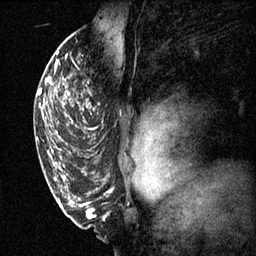
Breast MRI (dynamic contrast-enhanced), one sagittal slice. 3 images stored at this slice position (order not interpretable as contrast timing). 1.5 T. TE 4.2 ms, TR 11.1 ms. 256 × 256 image matrix, field of view 180 × 180 mm. Patient: female, 50 years.
Outlined on this slice (semi-automatically segmented with operator editing):
- analysis volume of interest (the breast-tissue region the enhancement analysis was run in; not a lesion): bounding box [x1, y1, x2, y2] px = [68, 68, 104, 141]
- tumour enhancement mask (voxels above the 70 % enhancement threshold inside the analysis volume of interest): [68, 92, 92, 129]